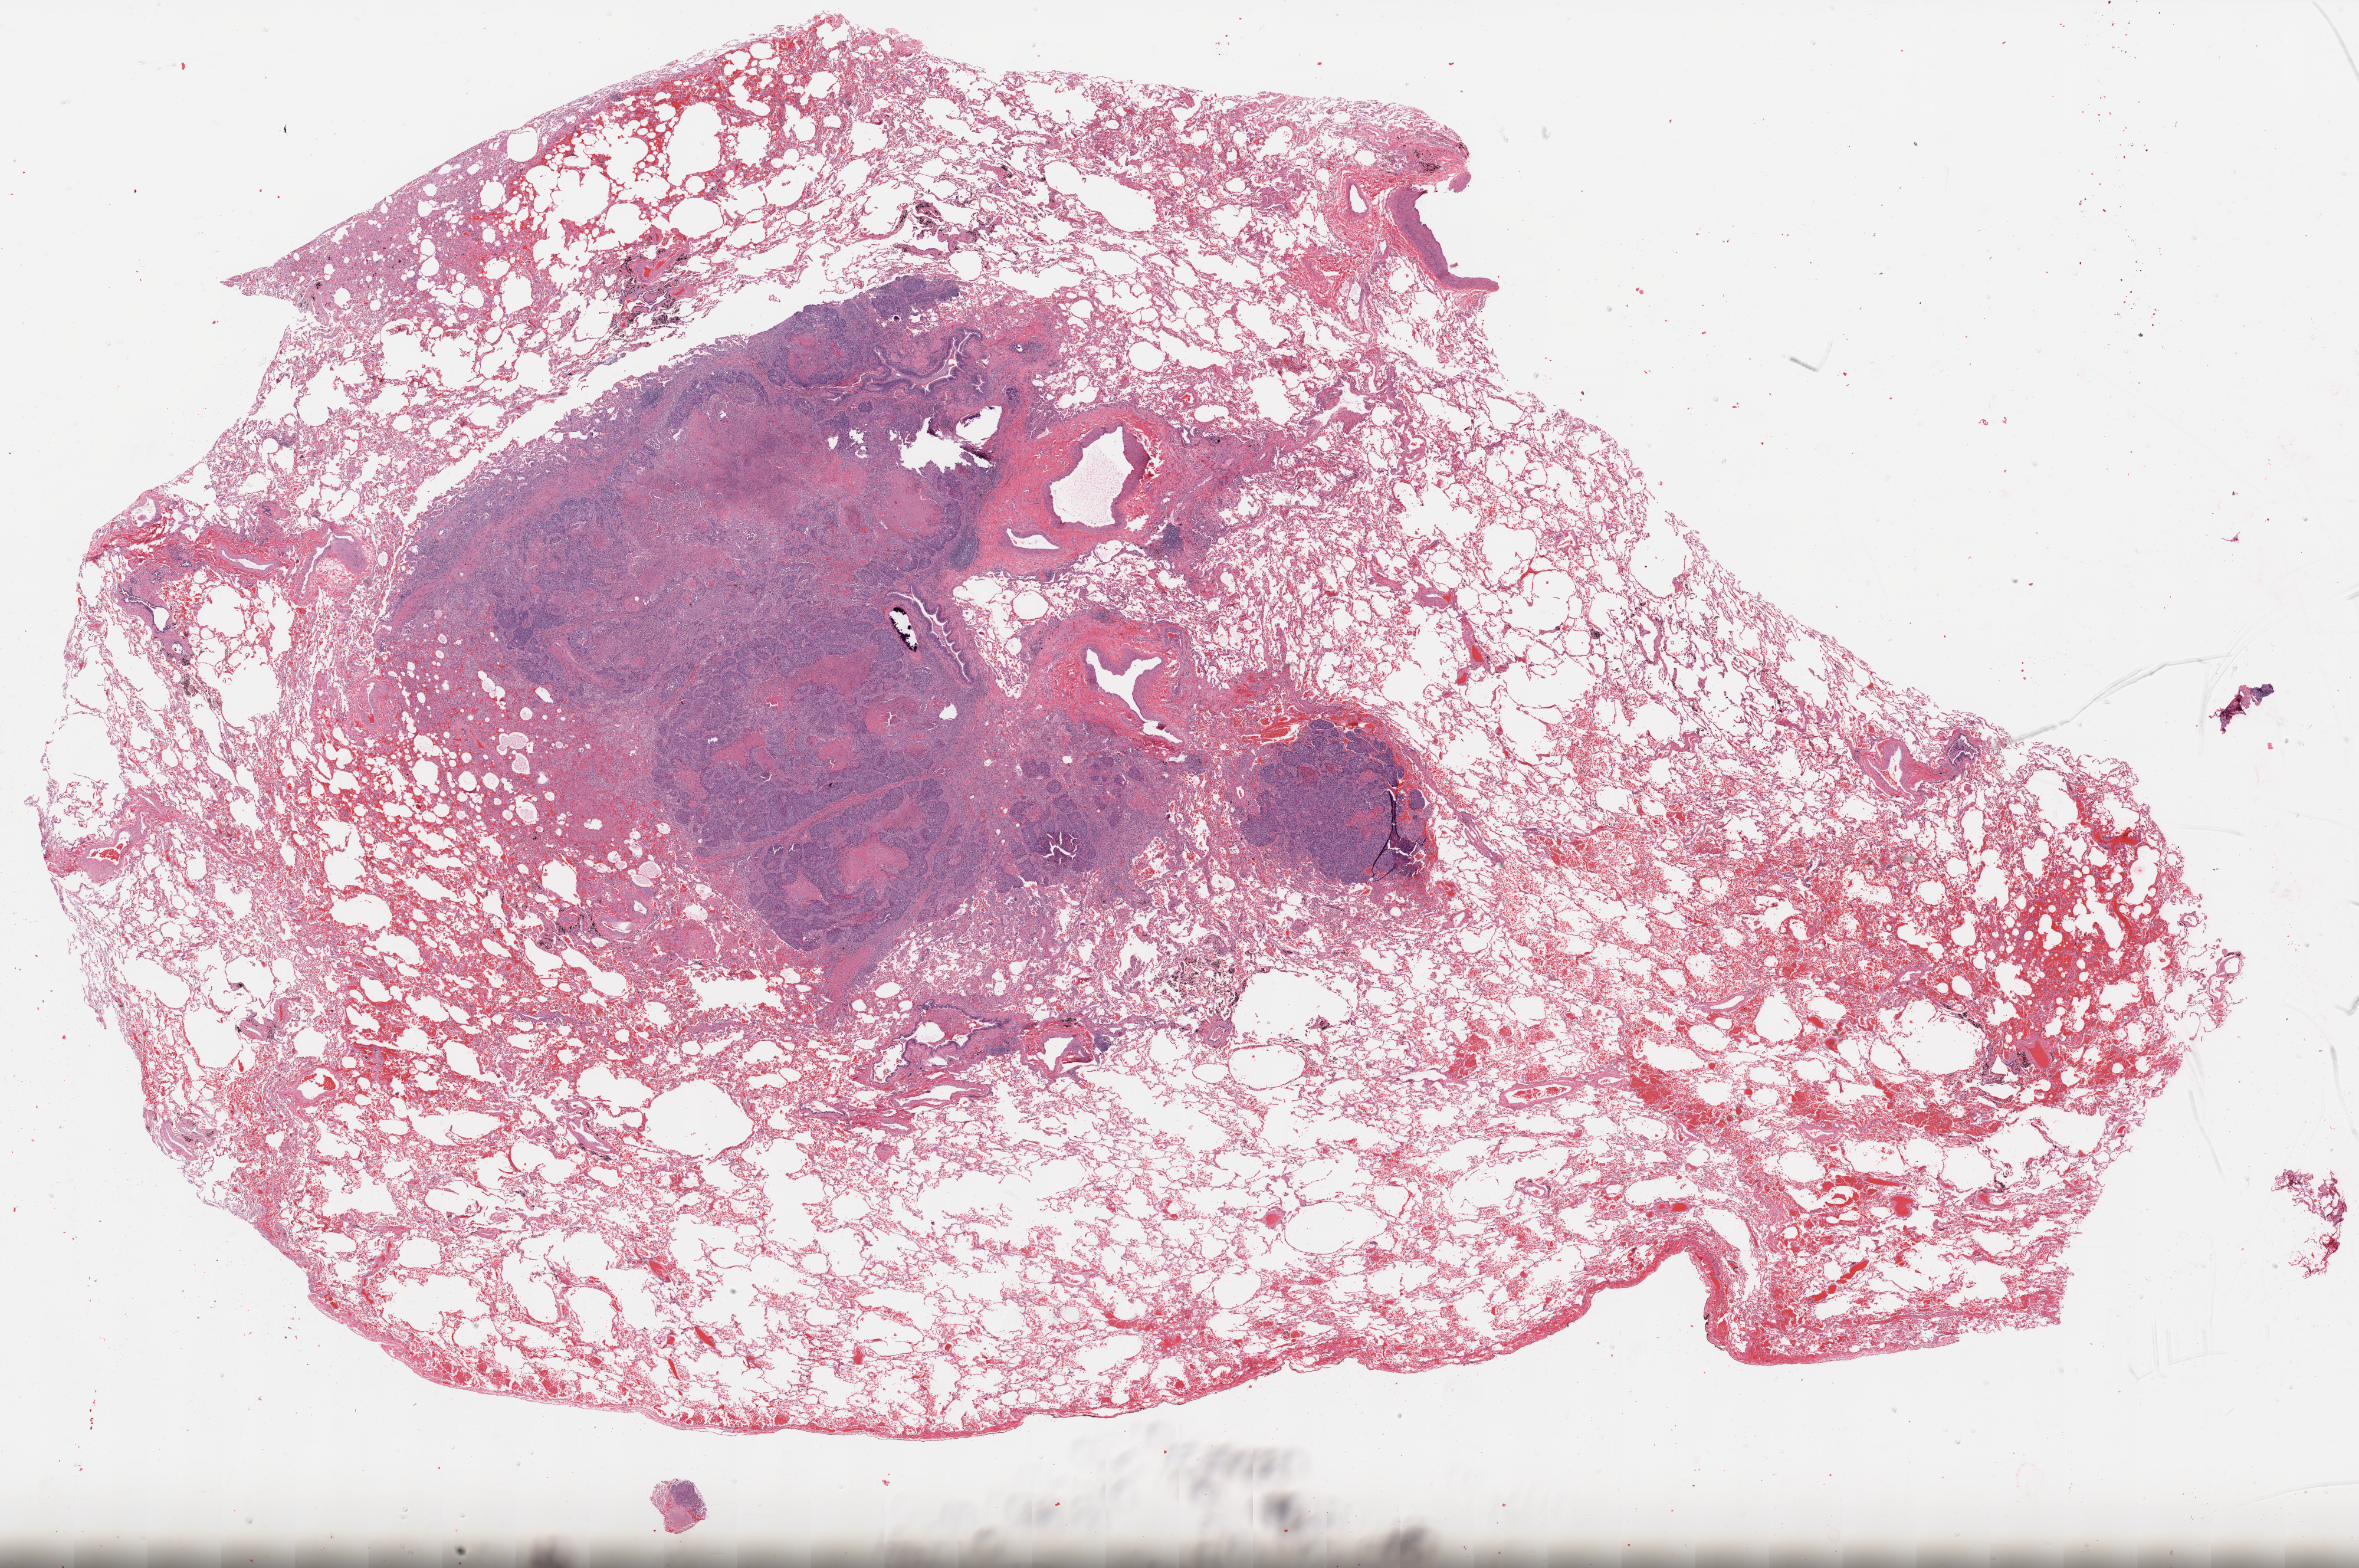
Digitized H&E-stained tissue section (whole slide), a low-resolution overview of the entire scanned area, about 32.1 x 21.4 mm (slide scanned at 20x). FFPE section. Primary tumour sample from the lung. Patient: female, age at initial diagnosis 79 years.
Diagnosis: Squamous cell carcinoma, NOS.